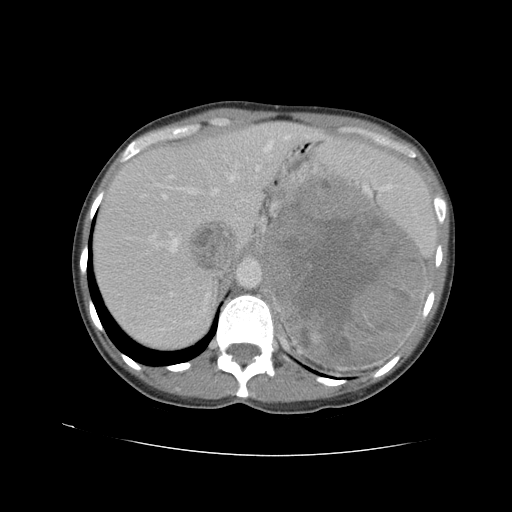
Contrast-enhanced abdominal CT, one axial slice. Position 73 of 90 along the scan axis. Reconstruction kernel STANDARD. 120 kVp. Soft-tissue window (W 400 / L 40 HU). 512 × 512 image matrix. Female patient. From the clinical record (not read from this slice): diagnosis: adrenocortical carcinoma; tumour side: left adrenal; tumour size at pathology: 18 cm; Ki-67 index: 11 %.
Outlined on this slice (semi-automatically segmented with operator editing):
- mass: bounding box (x1, y1, x2, y2) in pixels: (268, 180, 425, 368)